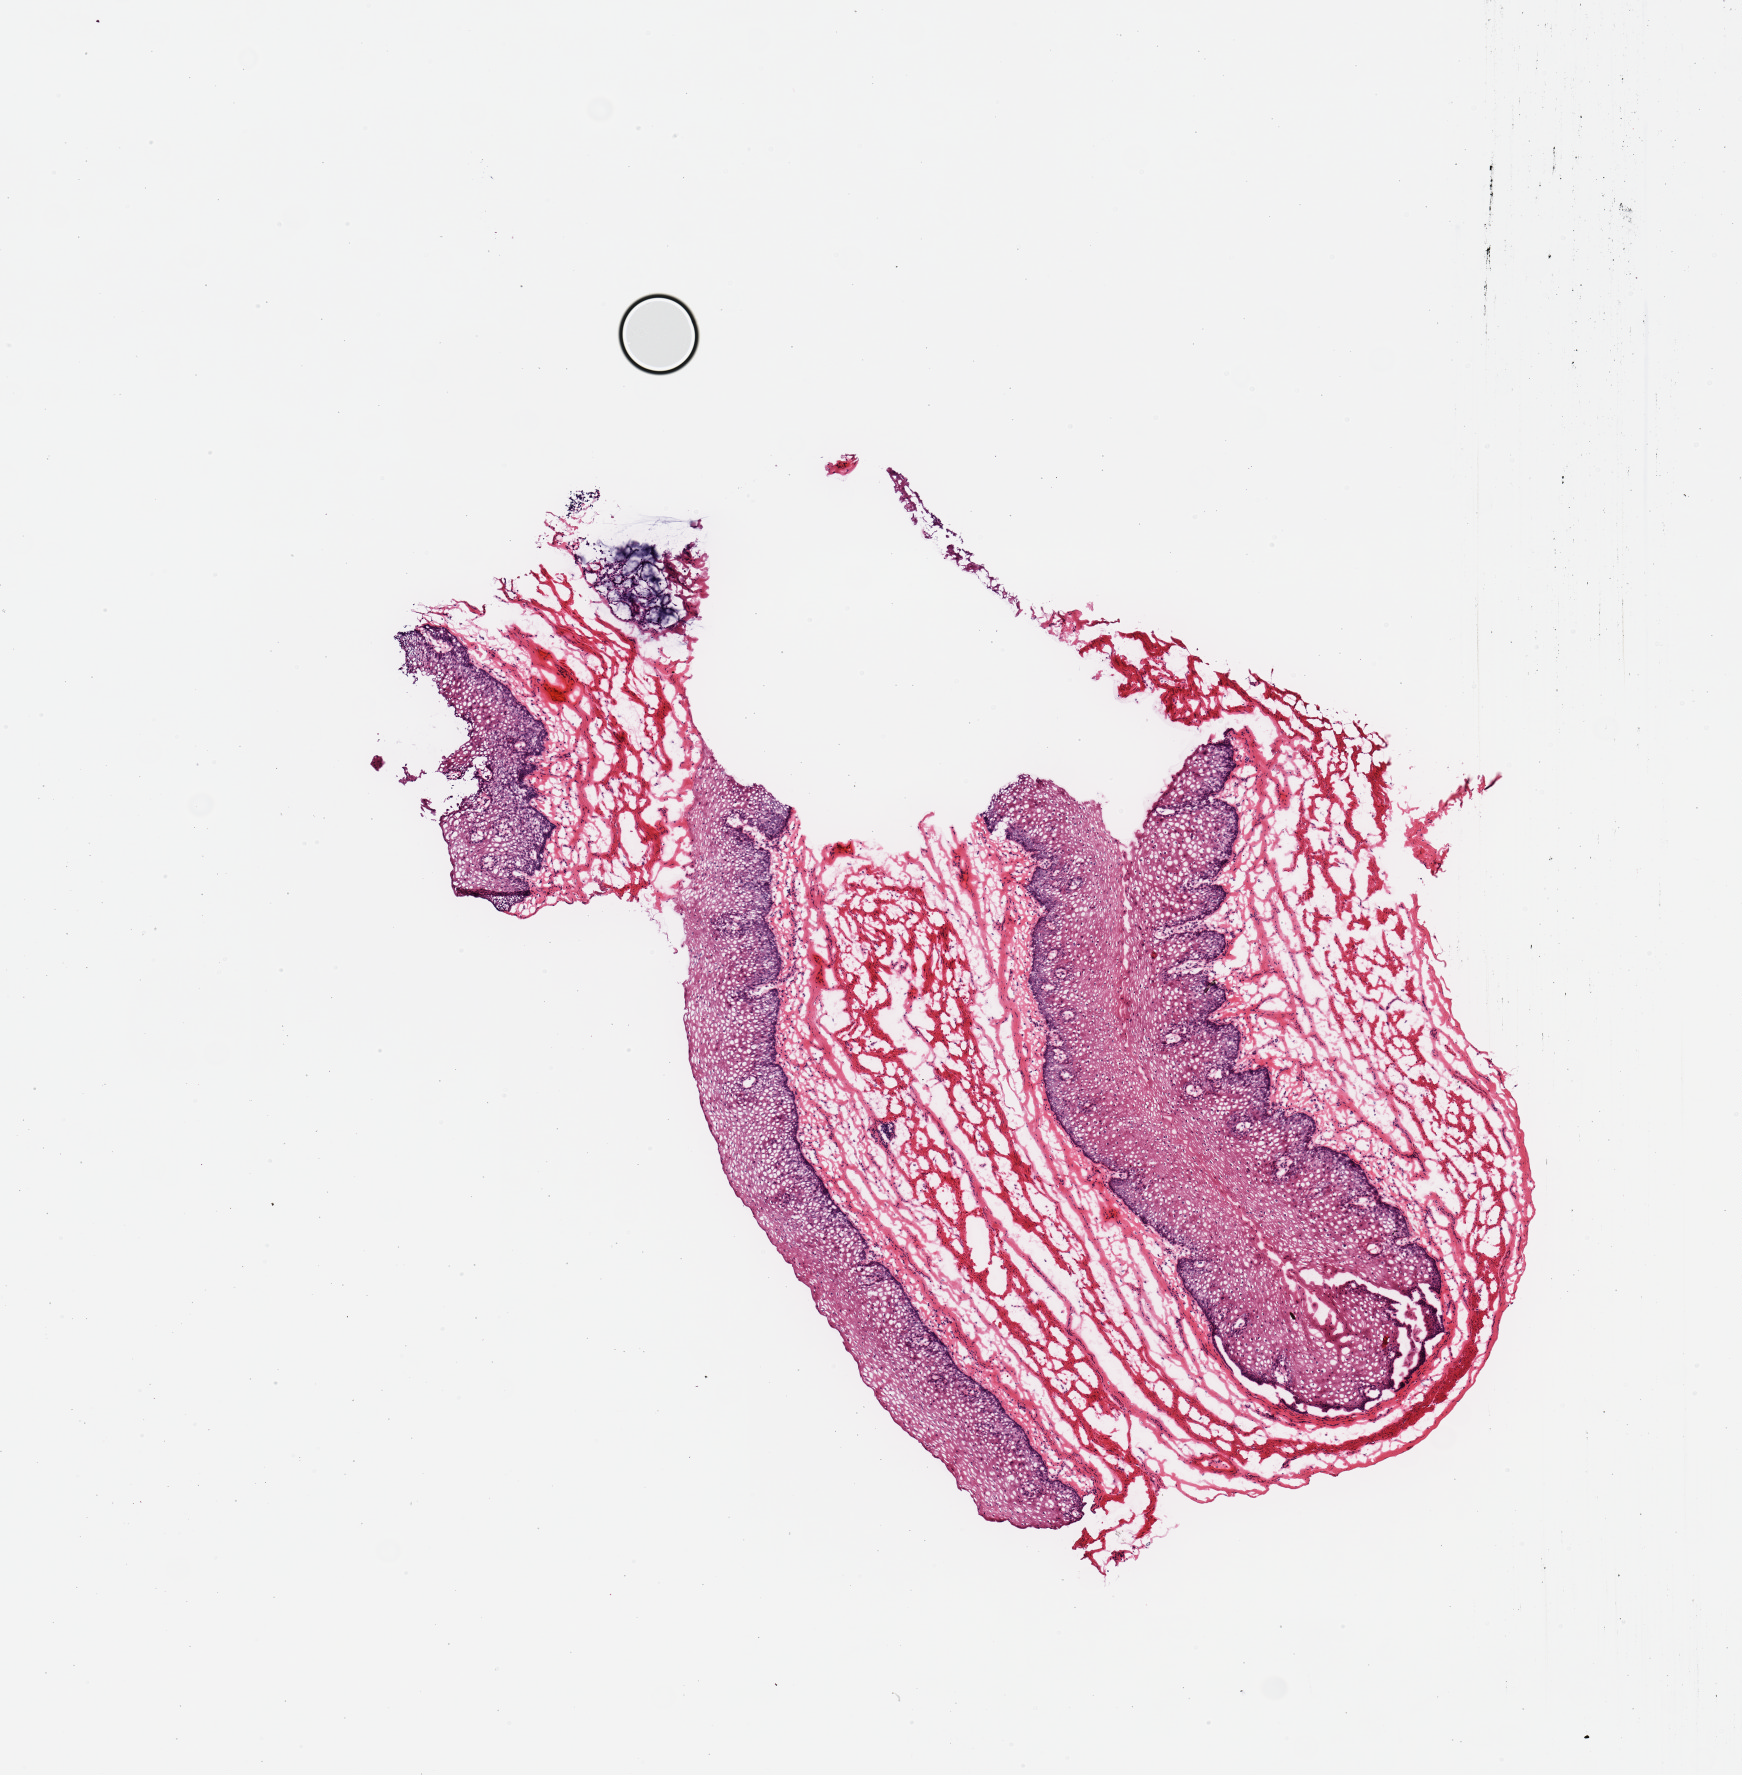
Haematoxylin and eosin whole-slide image, brightfield — a low-resolution overview of the entire scanned area, about 6.9 x 7.0 mm (from a 20x scan). Frozen section. Target tissue: esophageal mucous membrane. Donor tissue sample. Donor: male.
Review note (as recorded): 1 piece.